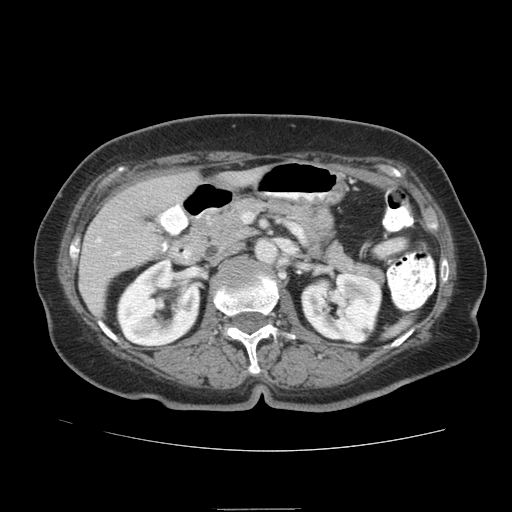
Contrast-enhanced abdominal CT (liver protocol), one axial slice. Slice 34 of 95 in the series (ordered by position). Reconstruction kernel STANDARD. 140 kVp. Soft-tissue window (W 400 / L 40 HU). 2.5 mm slice thickness. 512 × 512 image matrix. Case-level facts recorded for this patient, not image findings: diagnosis: hepatocellular carcinoma (patient treated with transarterial chemoembolisation; whether this scan precedes or follows treatment is not stated here); TNM stage (as recorded): Stage-IVA; Child-Pugh class: B; tumour differentiation: moderately differentiated; tumour nodularity: uninodular.
Outlined on this slice (semi-automatic segmentation, software-assisted and operator-edited):
- liver parenchyma outside the tumour (the mass and vessels are separate outlines, so this box may not span the whole liver): box from (x=79, y=166) to (x=265, y=310) px
- liver vessels: (x=96, y=239)–(x=120, y=256)